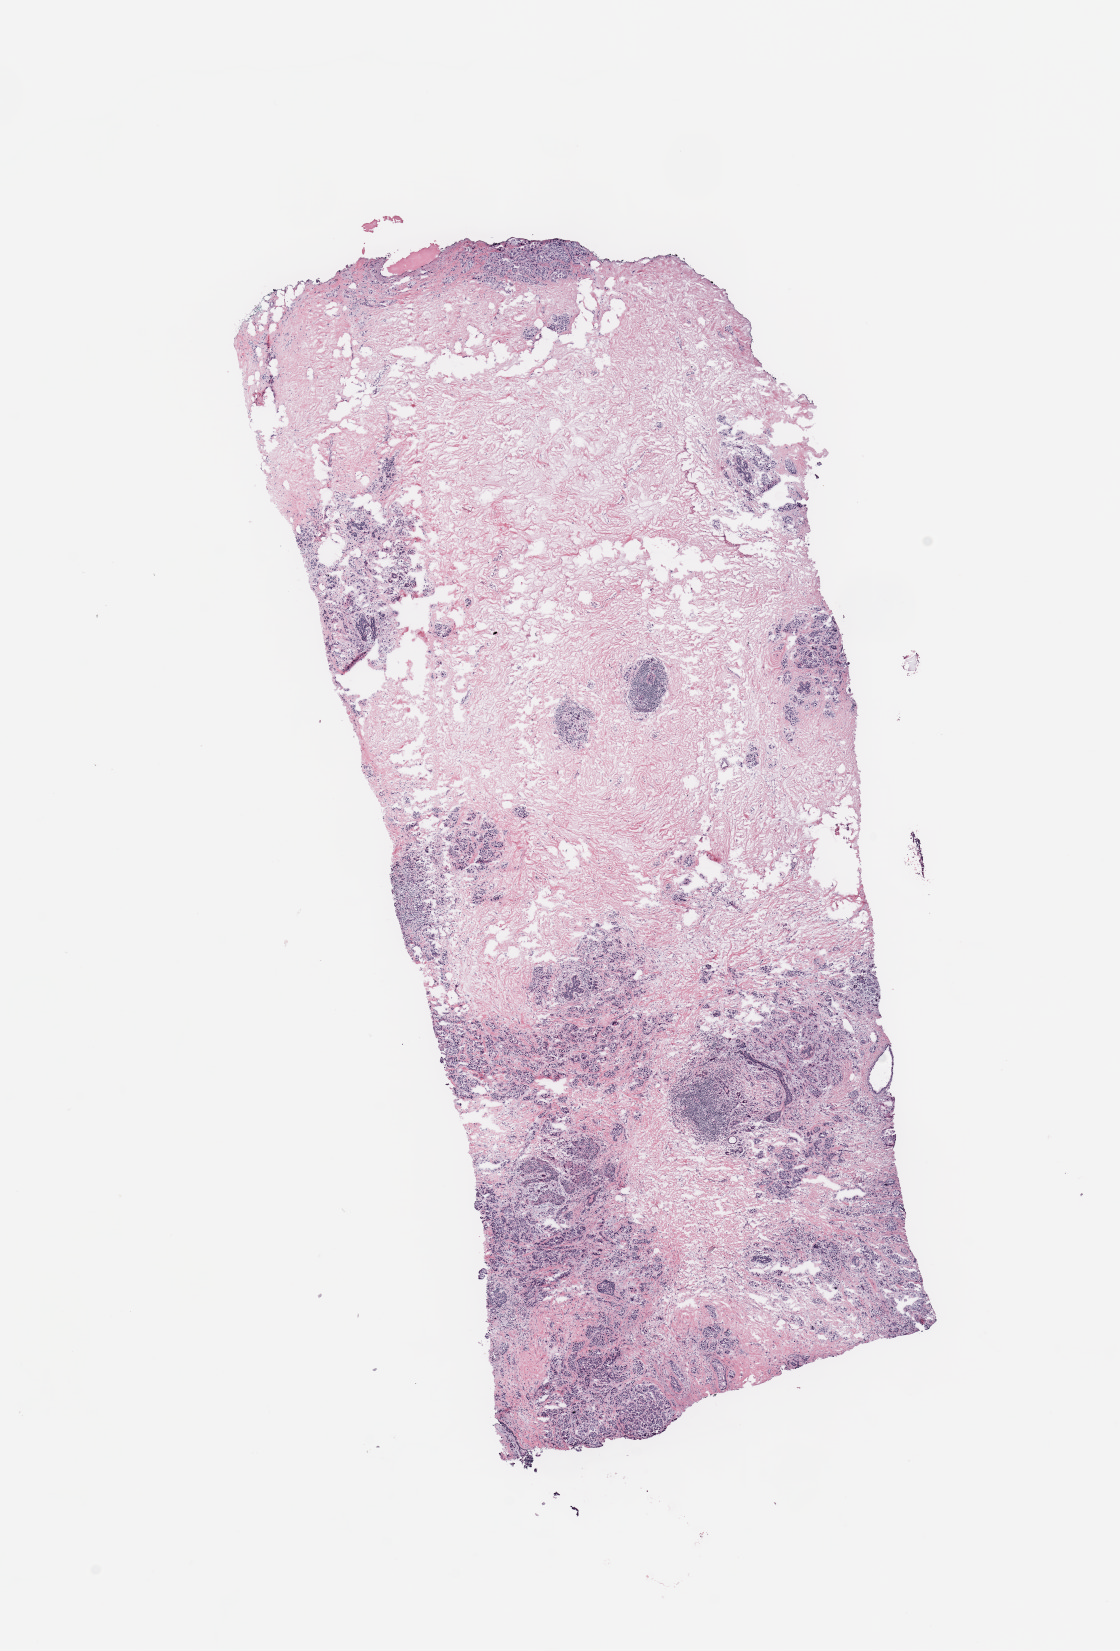
H&E whole-slide image, whole scanned area (about 8.9 x 13.1 mm, from a 20x scan) shown as a low-resolution overview; breast, tissue type not recorded.
Patient diagnosis (cohort enrolment): breast cancer (breast).